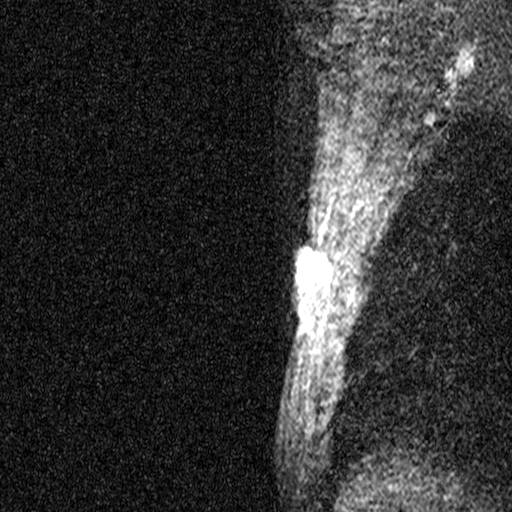
Breast MRI (dynamic contrast-enhanced), one sagittal slice. Slice 35 of 44 in the series (ordered by position). Dynamic contrast-enhanced study with each time point stored as its own series, time point 2 of 3 at this slice position (early post-contrast, ordered by acquisition time). 1.5 T. TE 4.5 ms, TR 11 ms. 512 × 512 image matrix, field of view 200 × 200 mm. Patient: female, 45 years. Case-level facts recorded for this patient, not image findings: setting: breast cancer imaged before/during neoadjuvant chemotherapy; receptor status: HR-positive, HER2-negative.
Outlined on this slice (semi-automatically segmented with operator editing):
- analysis volume of interest (the breast-tissue region the enhancement analysis was run in; not a lesion): bounding box (x1, y1, x2, y2) in pixels: (256, 218, 338, 359)
- tumour enhancement mask (voxels above the 90 % enhancement threshold inside the analysis volume of interest): (295, 252, 329, 292)